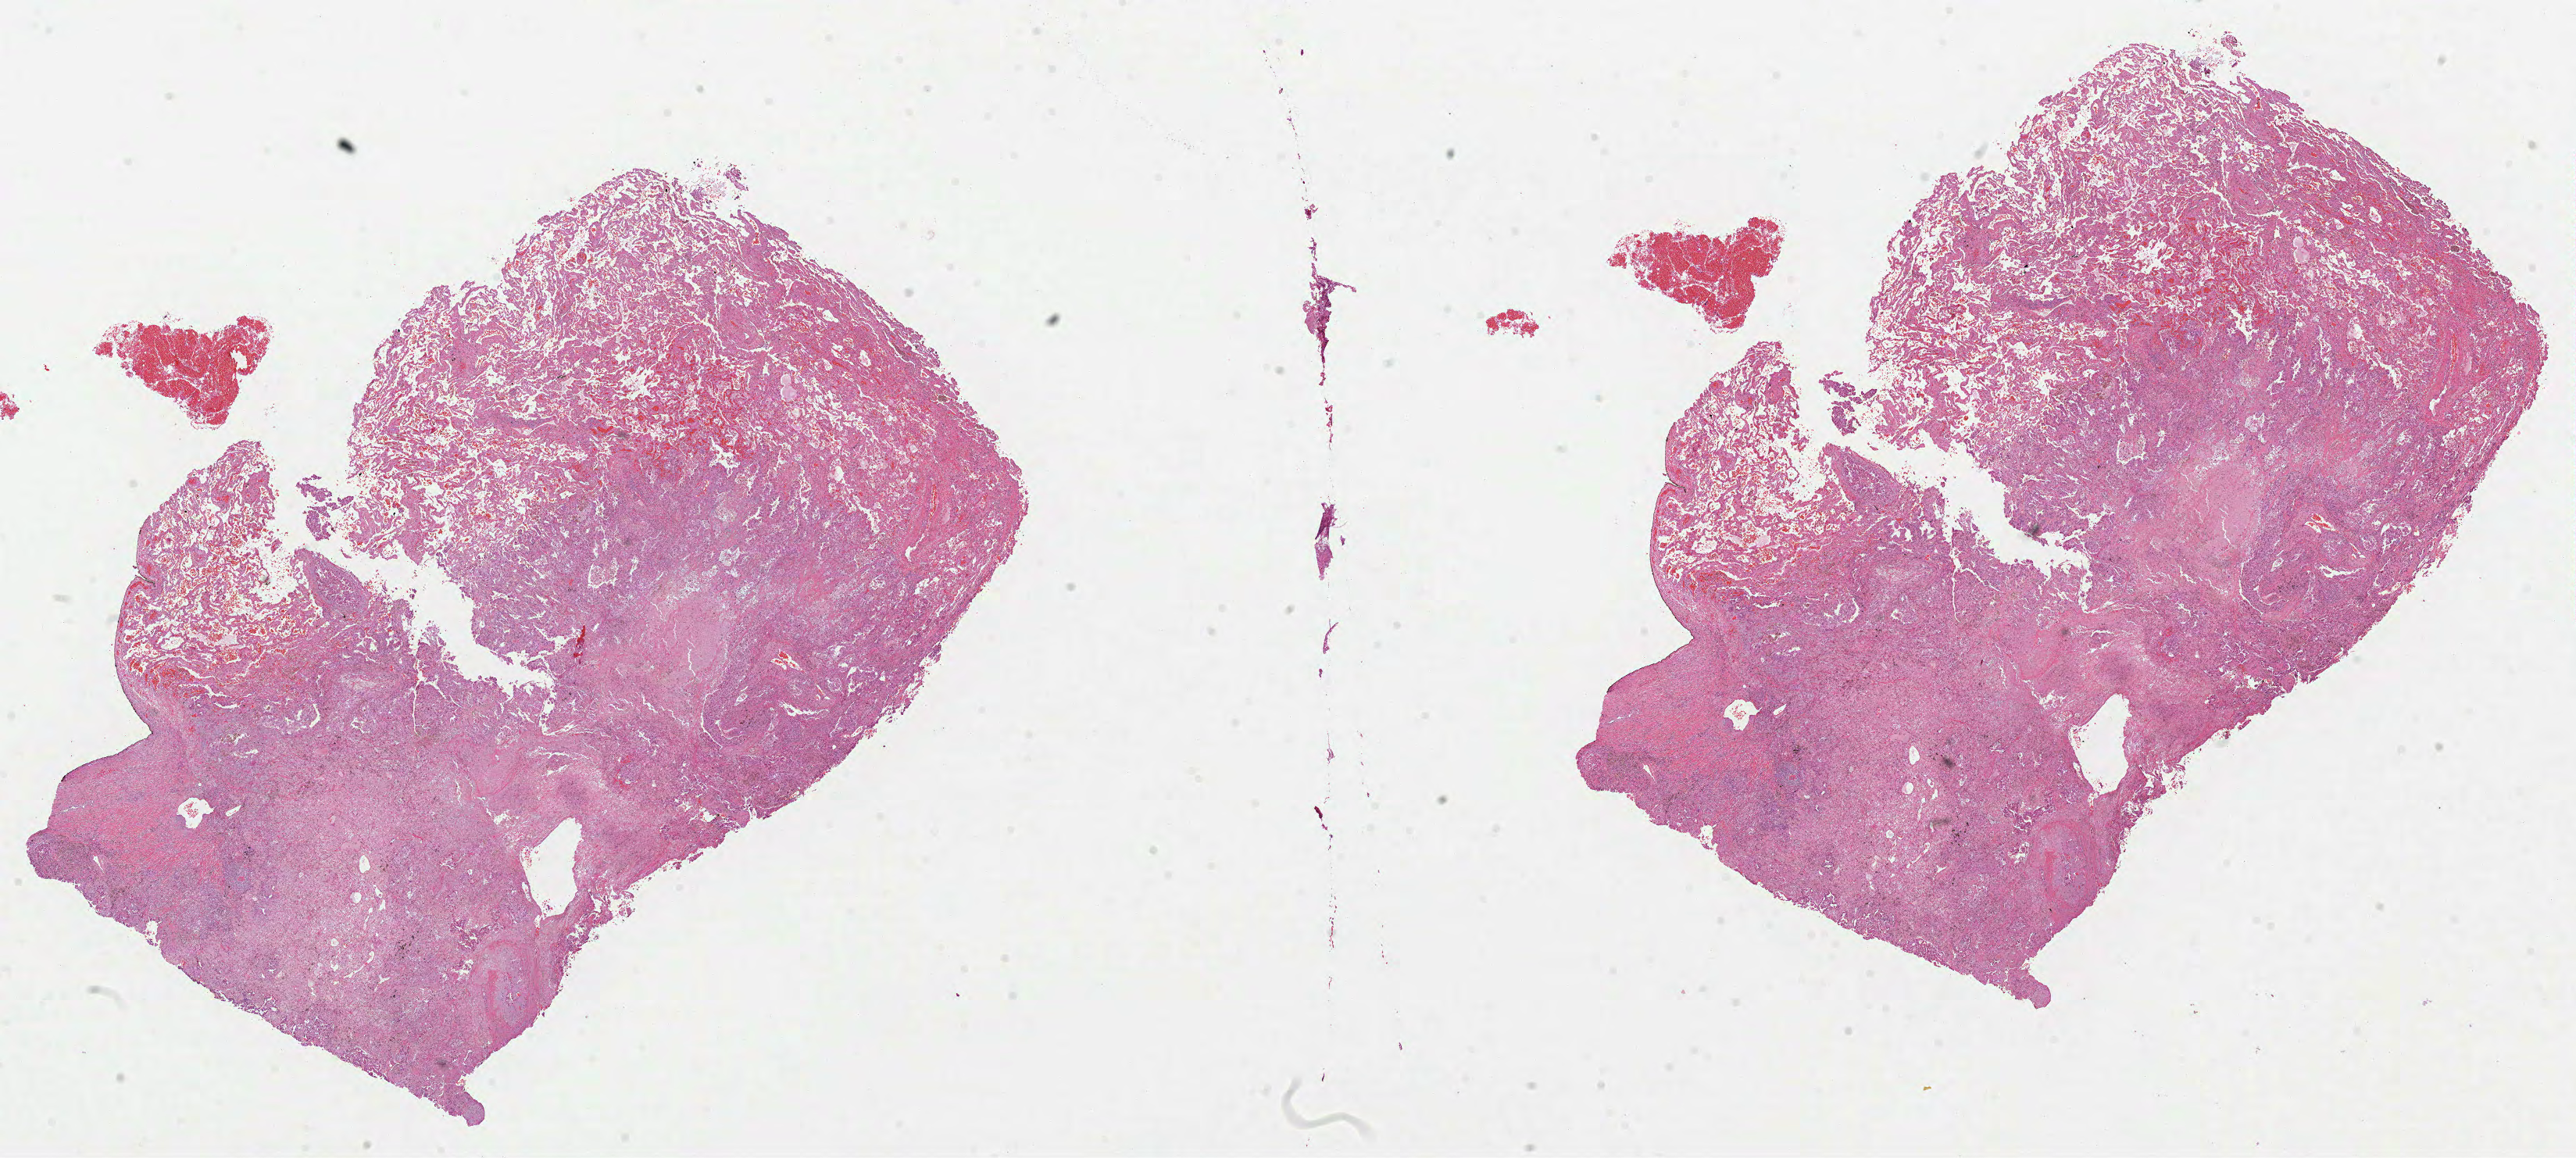
Hematoxylin and eosin (H&E) stained whole-slide image — shown as a low-resolution overview of the whole scanned area (about 26.6 x 12.0 mm, slide scanned at 40x); FFPE section; primary tumour sample from the lung. Patient: female, age at initial diagnosis 60 years.
Laterality: right. AJCC pathologic stage: IIIB. Diagnosis: Adenocarcinoma with mixed subtypes.